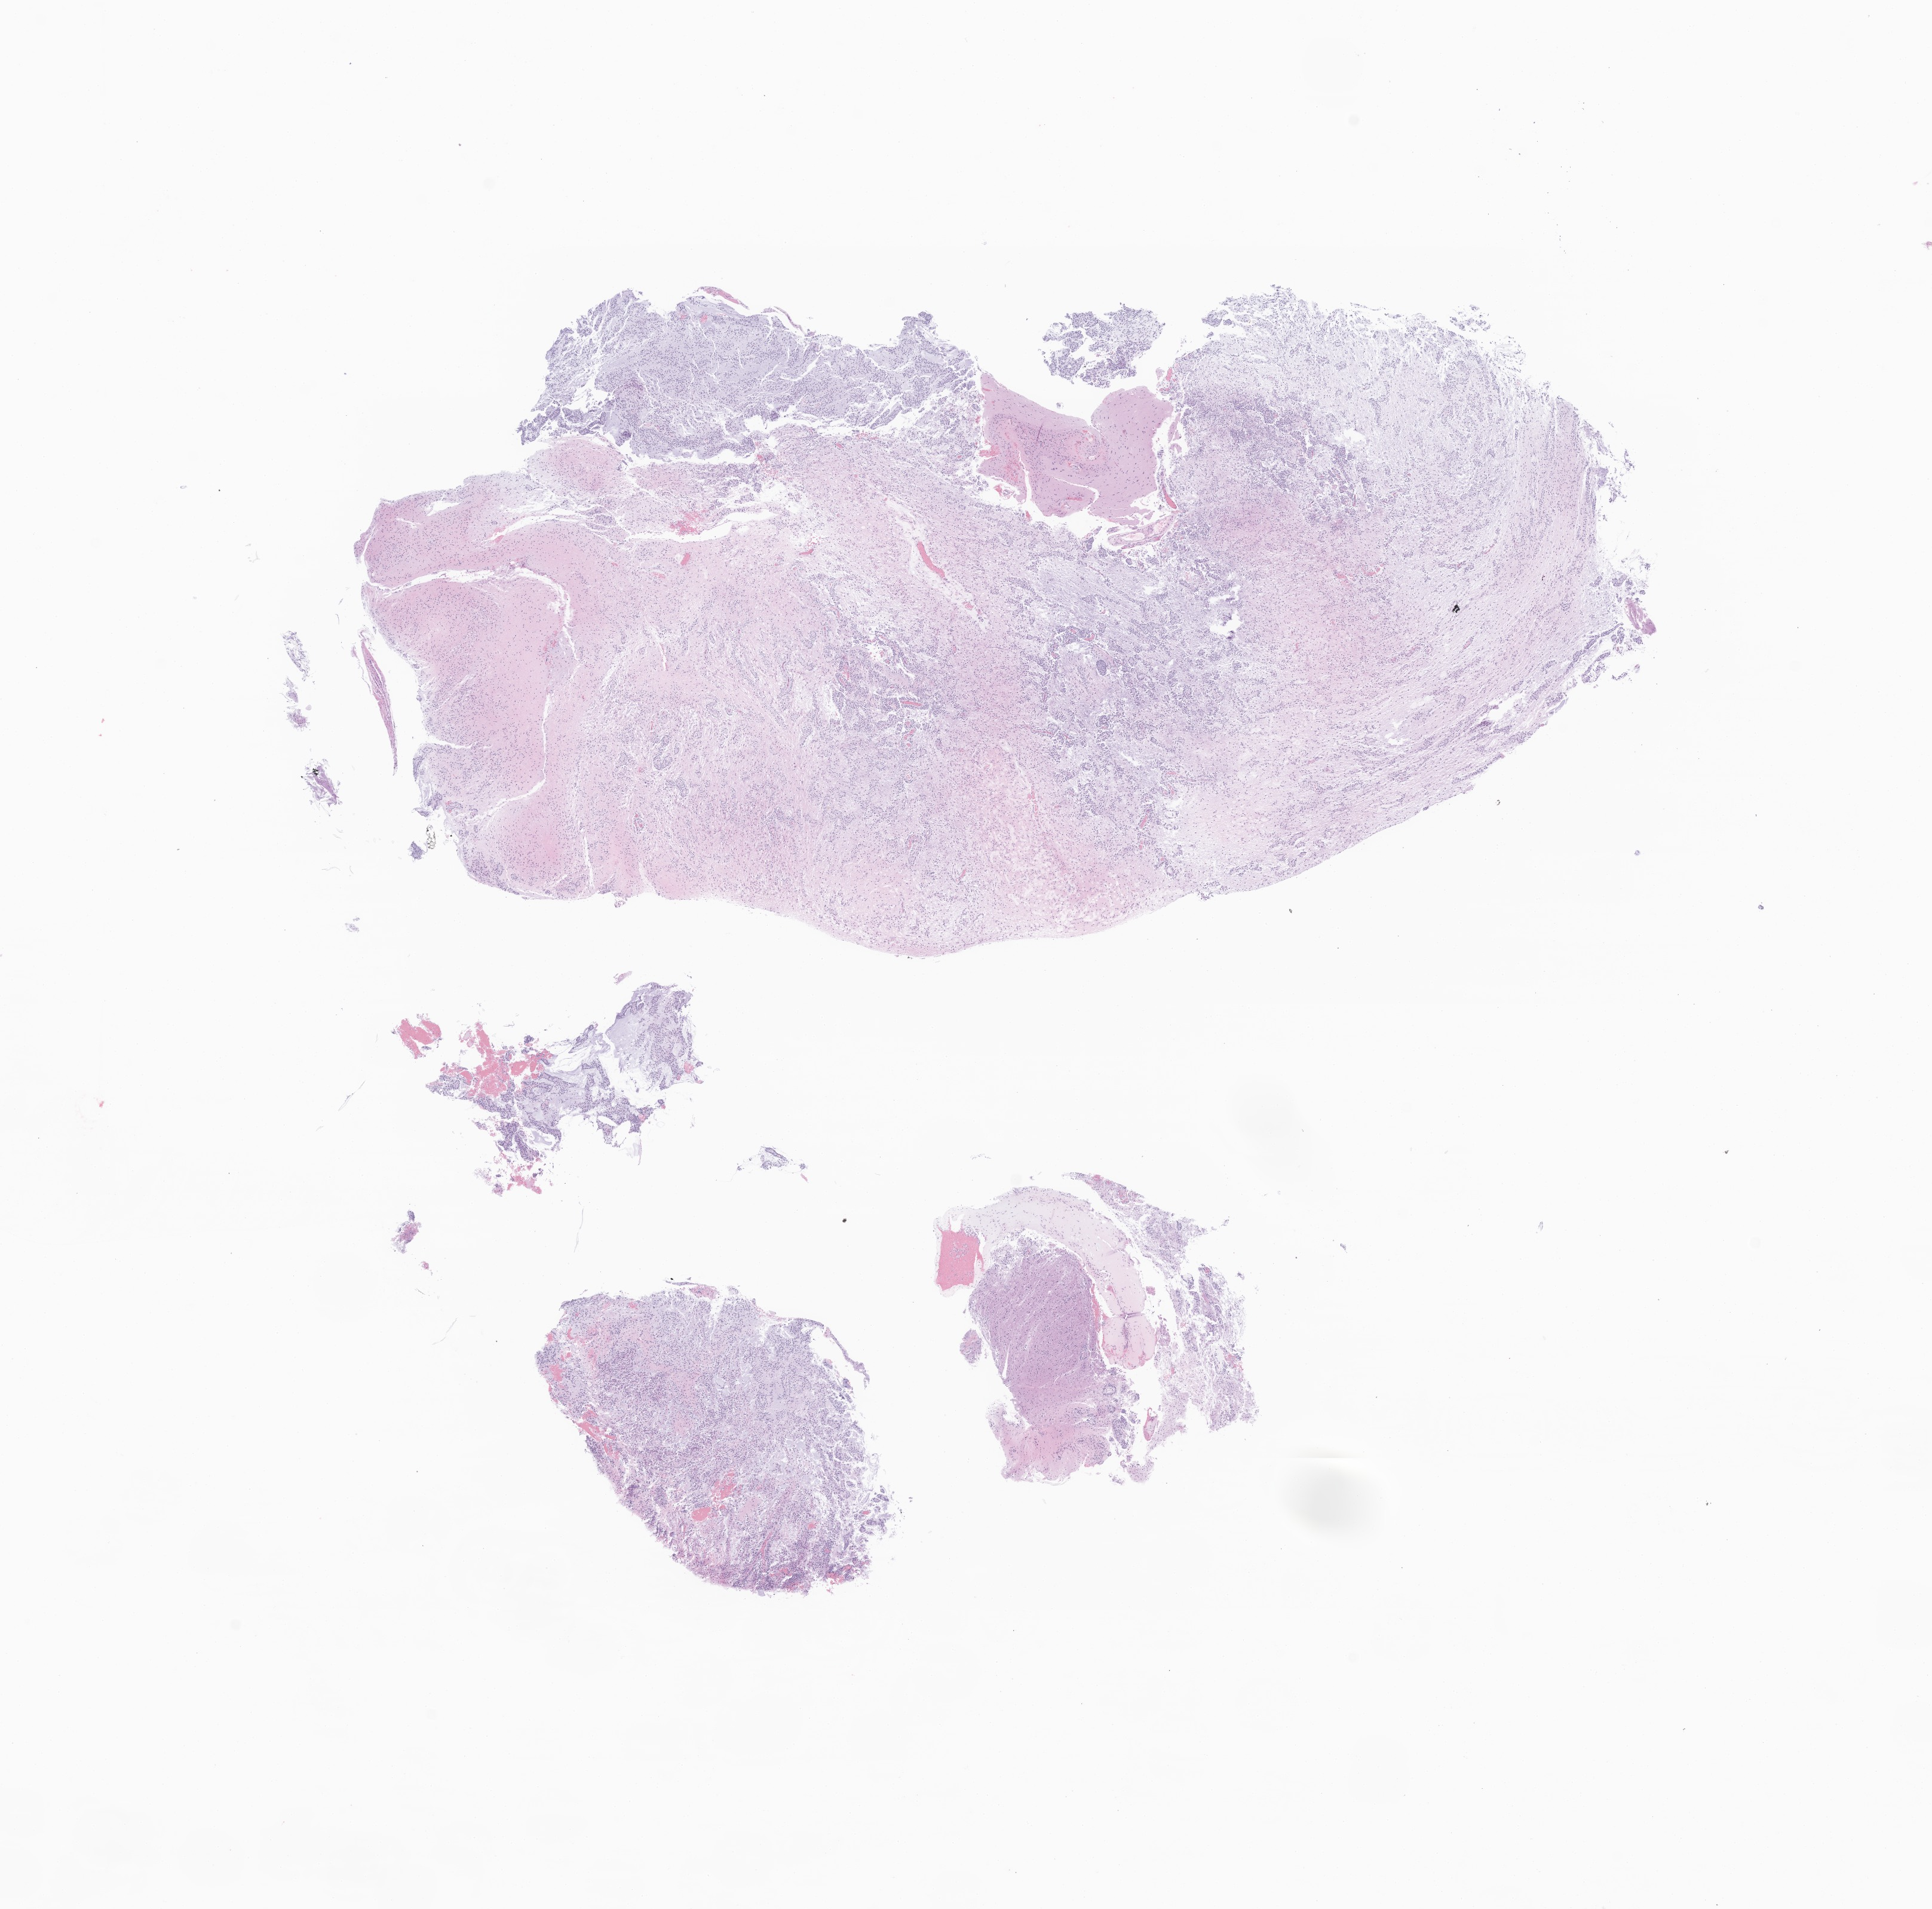
Whole-slide image, H&E stain of tumor tissue from the brain, low-resolution overview of the scanned area, about 13.6 x 13.5 mm. FFPE section. Patient female; age 191 months (15 years 11 months).
• diagnosis (ICD-O-3 morphology term): Glioma, malignant